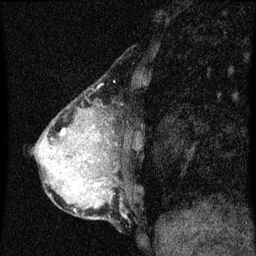
Breast MRI (dynamic contrast-enhanced), one sagittal slice; slice 17 of 60 in the series (ordered by position); dynamic contrast-enhanced series, image 2 of 3 at this slice position (ordered by acquisition); 1.5 T; TE 4.2 ms, TR 8 ms; 2 mm slice thickness; 256 × 256 image matrix, field of view 180 × 180 mm. Patient: female, 49 years.
Structures marked on this image (semi-automatically segmented with operator editing):
- analysis volume of interest (the breast-tissue region the enhancement analysis was run in; not a lesion): bounding box (x1, y1, x2, y2) in pixels: (44, 174, 89, 201)
- tumour enhancement mask (voxels above the 70 % enhancement threshold inside the analysis volume of interest): (73, 184, 76, 187)